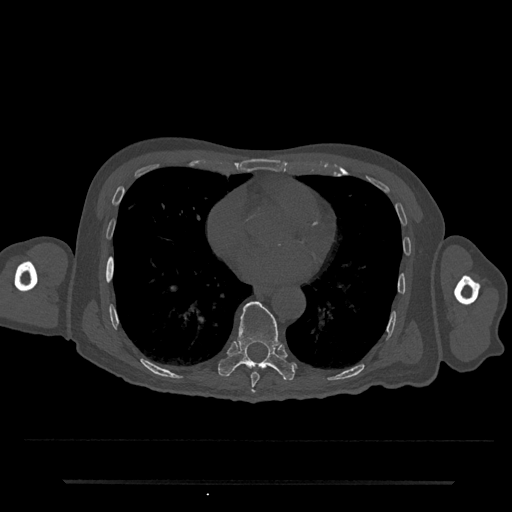
CT including the spine, one axial slice. Position 382 of 797 along the scan axis. 120 kVp. Bone window (W 1800 / L 400 HU). 512 × 512 image matrix, field of view 427 × 427 mm. Patient: male, 74 years. From the clinical record (not read from this slice): primary cancer: prostate.
Structures marked on this image (semi-automatically segmented with operator editing):
- T8 vertebra: bounding box (x1, y1, x2, y2) in pixels: (251, 372, 260, 393)
- T9 vertebra: (218, 301, 295, 380)